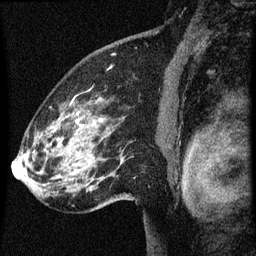
Breast MRI (dynamic contrast-enhanced), one sagittal slice. Dynamic contrast-enhanced series, image 2 of 3 at this slice position (ordered by acquisition). 1.5 T. TE 4.2 ms, TR 8 ms. 2 mm slice thickness. 256 × 256 image matrix, field of view 180 × 180 mm. Patient: female, 61 years.
Outlined on this slice (semi-automatic segmentation, software-assisted and operator-edited):
- analysis volume of interest (the breast-tissue region the enhancement analysis was run in; not a lesion): box from (x=27, y=90) to (x=134, y=209) px
- tumour enhancement mask (voxels above the 70 % enhancement threshold inside the analysis volume of interest): (x=33, y=100)–(x=79, y=153)